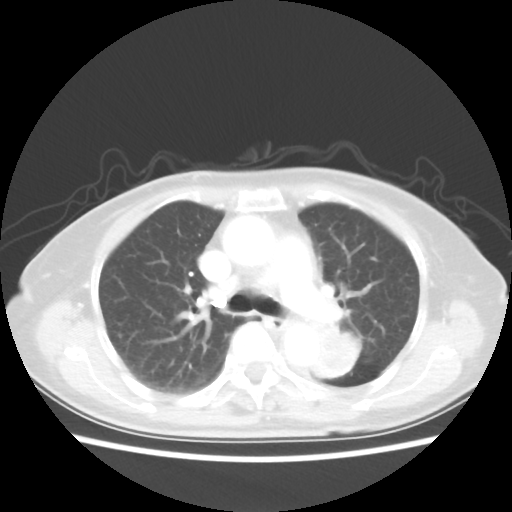
Chest CT, one axial slice. Slice 32 of 50 in the series (ordered by position). Reconstruction kernel STANDARD. 80 kVp. Lung window (W 1500 / L -600 HU). 512 × 512 image matrix, field of view 335 × 335 mm. Patient: female, 81 years. Case-level facts recorded for this patient, not image findings: clinical TNM (as recorded): T2 N0 M1a.
Annotated regions visible in this slice (rectangle marked by the reading radiologist):
- lung tumour (recorded histology: squamous cell carcinoma): bounding box (x1, y1, x2, y2) in pixels: (308, 323, 363, 382)